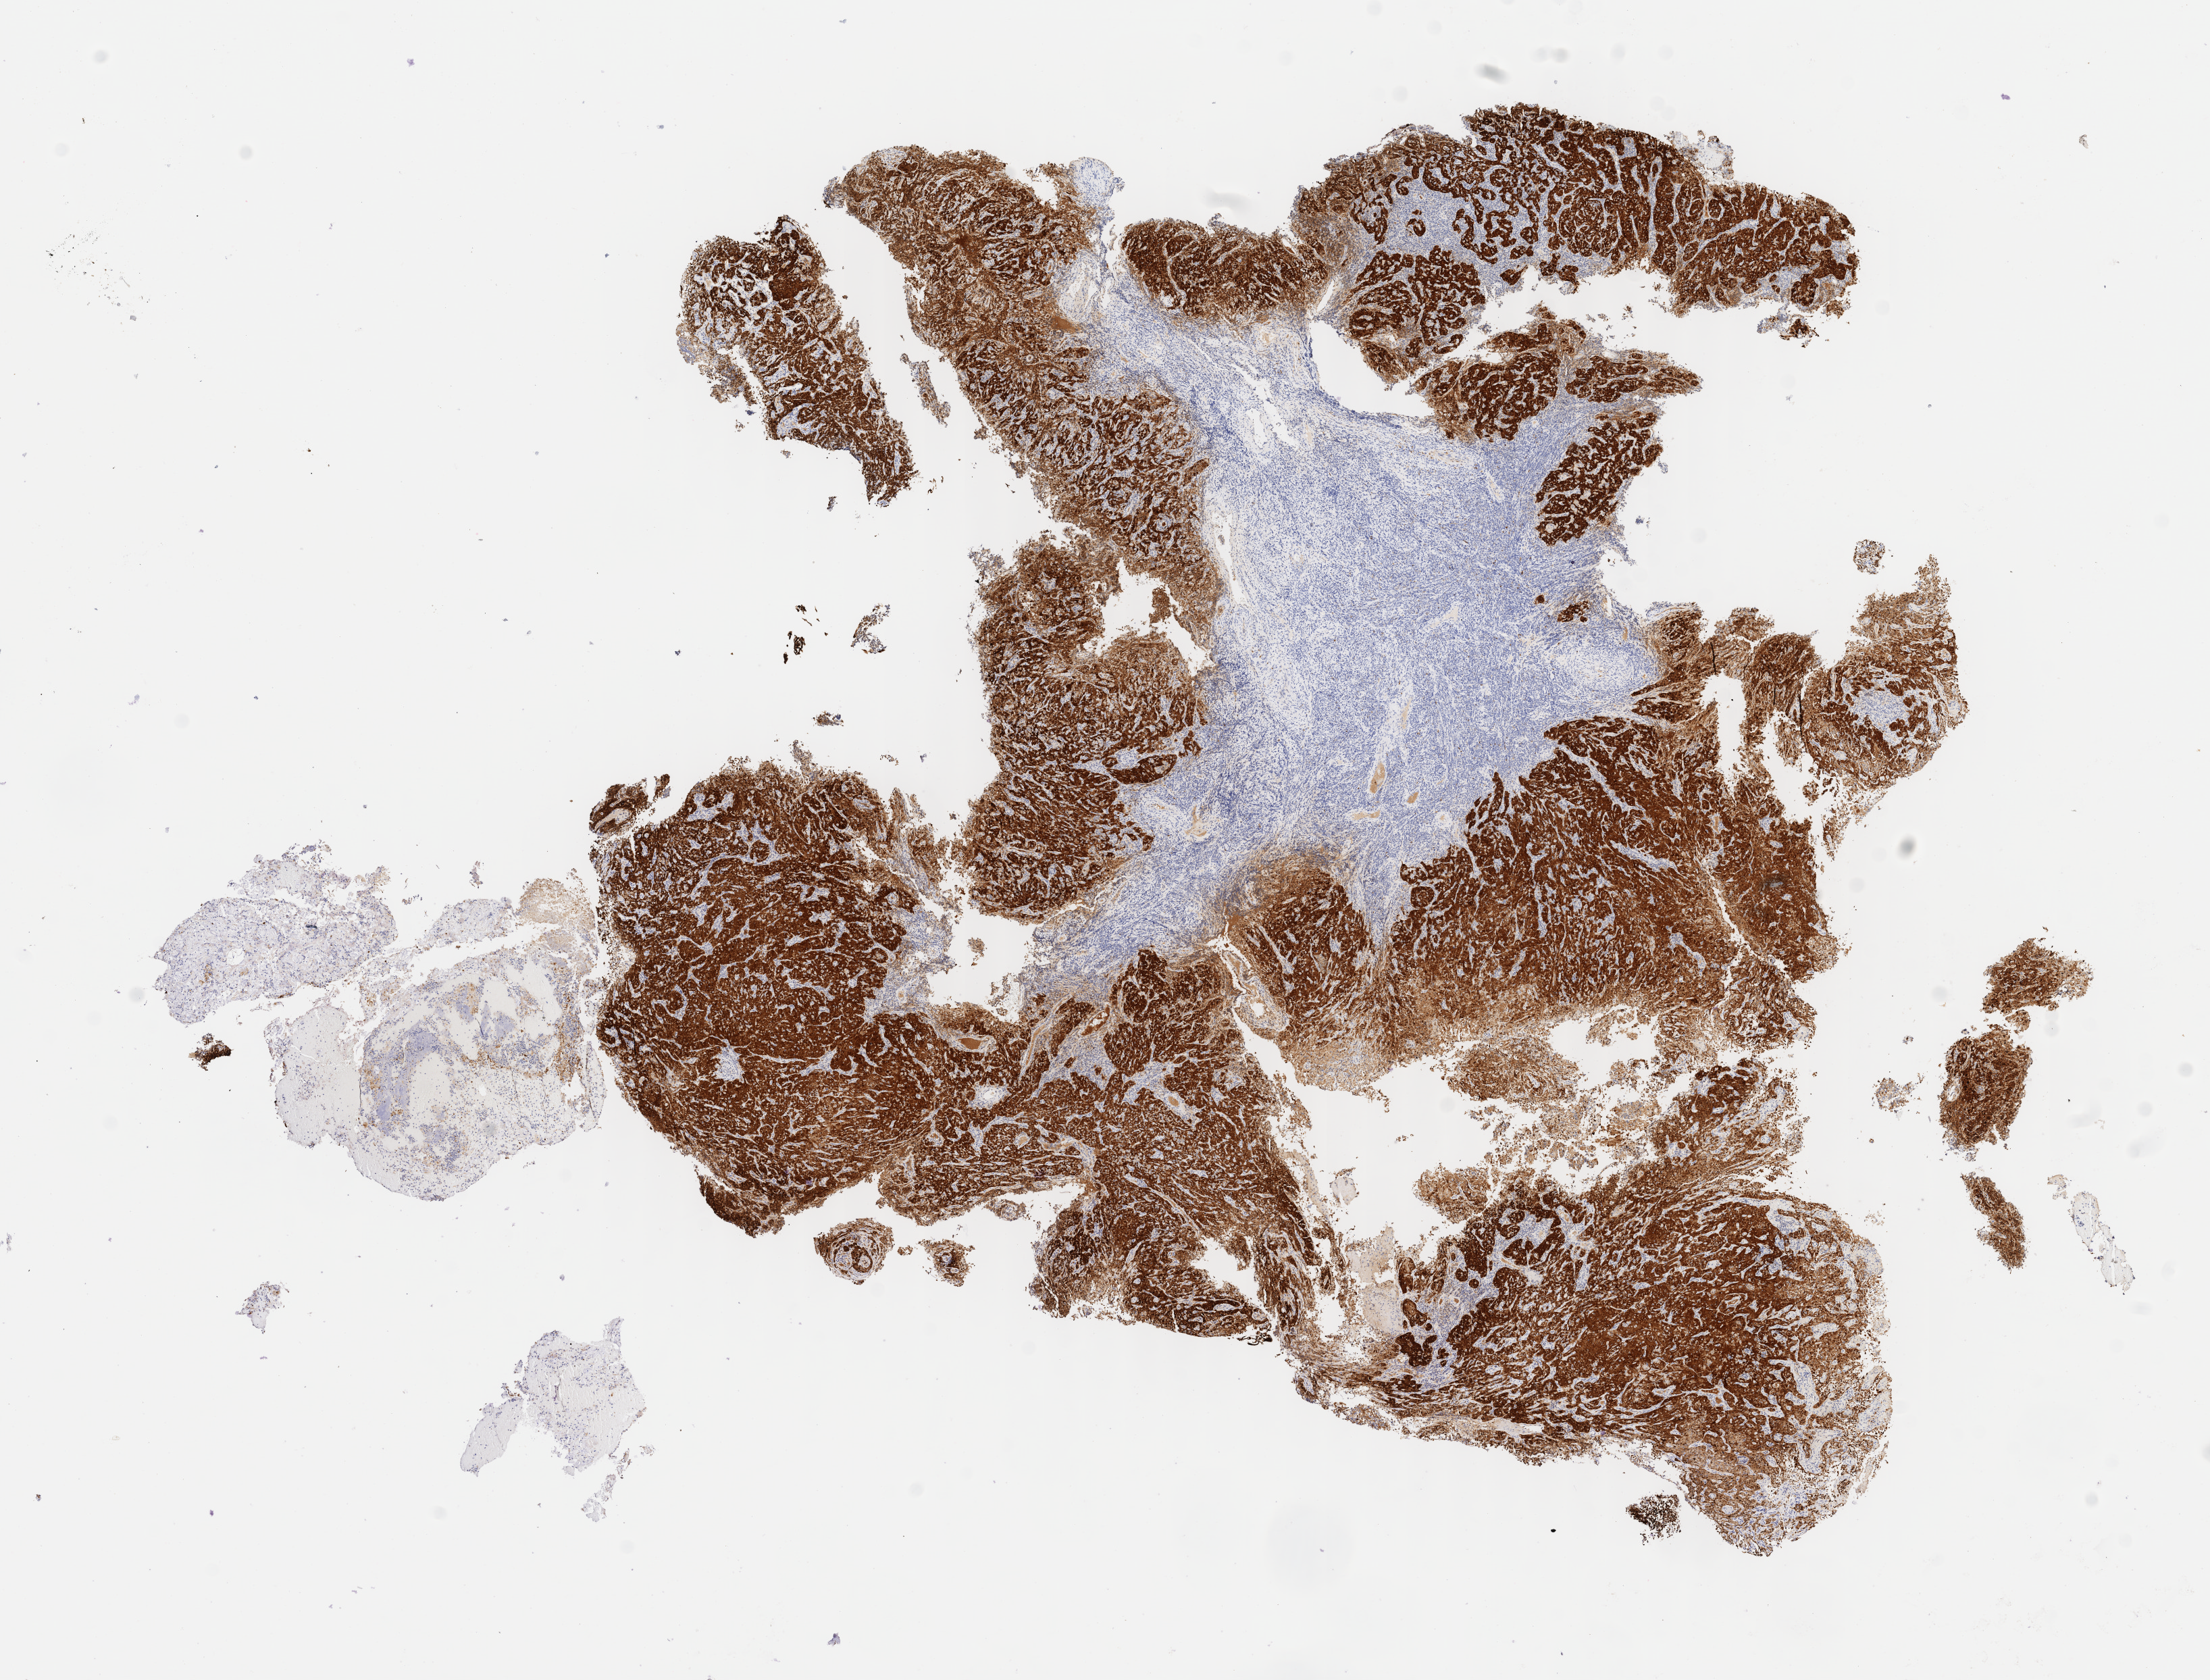
Whole-slide image, immunohistochemical stain for p16 (p16INK4a) — a low-resolution overview of the entire scanned area, about 13.0 x 9.9 mm. Specimen: tumor tissue. Site: cervix. Patient: female, age 32 years.
Histologic diagnosis: Squamous cell carcinoma, large cell, nonkeratinizing, NOS.